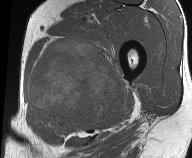
MRI of an extremity soft-tissue mass, one axial slice. Slice 30 of 61 in the series (ordered by position). MR volume resampled by the dataset authors to the PET/CT grid (not the native acquisition matrix). 192 × 158 image matrix, field of view 187 × 154 mm. Male patient. Case-level facts recorded for this patient, not image findings: histological type: pleiomorphic liposarcoma; grade: high; site of the primary tumour: left thigh.
Outlined on this slice (expert contour drawn on MRI and transferred to this co-registered scan by the dataset authors):
- gross tumour volume including surrounding oedema: bounding box [x1, y1, x2, y2] px = [27, 35, 126, 134]
- gross tumour volume (mass): [29, 39, 122, 127]